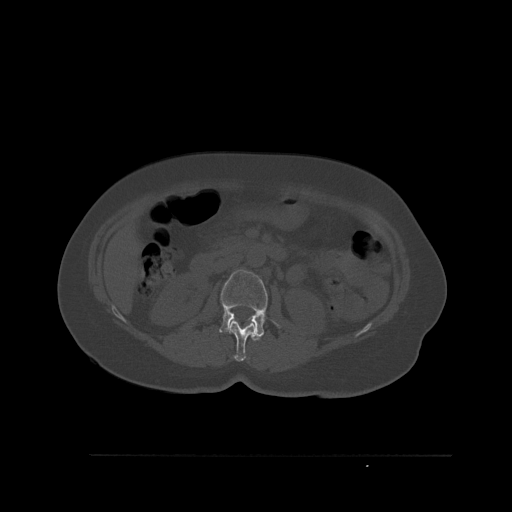
CT including the spine, one axial slice. Slice 253 of 527 in the series (ordered by position). Bone window (W 1800 / L 400 HU). 1.5 mm slice thickness. 512 × 512 image matrix, field of view 470 × 470 mm. Patient: female, 73 years. Case-level facts recorded for this patient, not image findings: primary cancer: breast; vertebrae with lytic lesions (as recorded): L2.
Outlined on this slice (semi-automatic segmentation, software-assisted and operator-edited):
- L1 vertebra: bounding box <228,320,256,362> (left, top, right, bottom; pixels)
- L2 vertebra: <219,269,280,341>